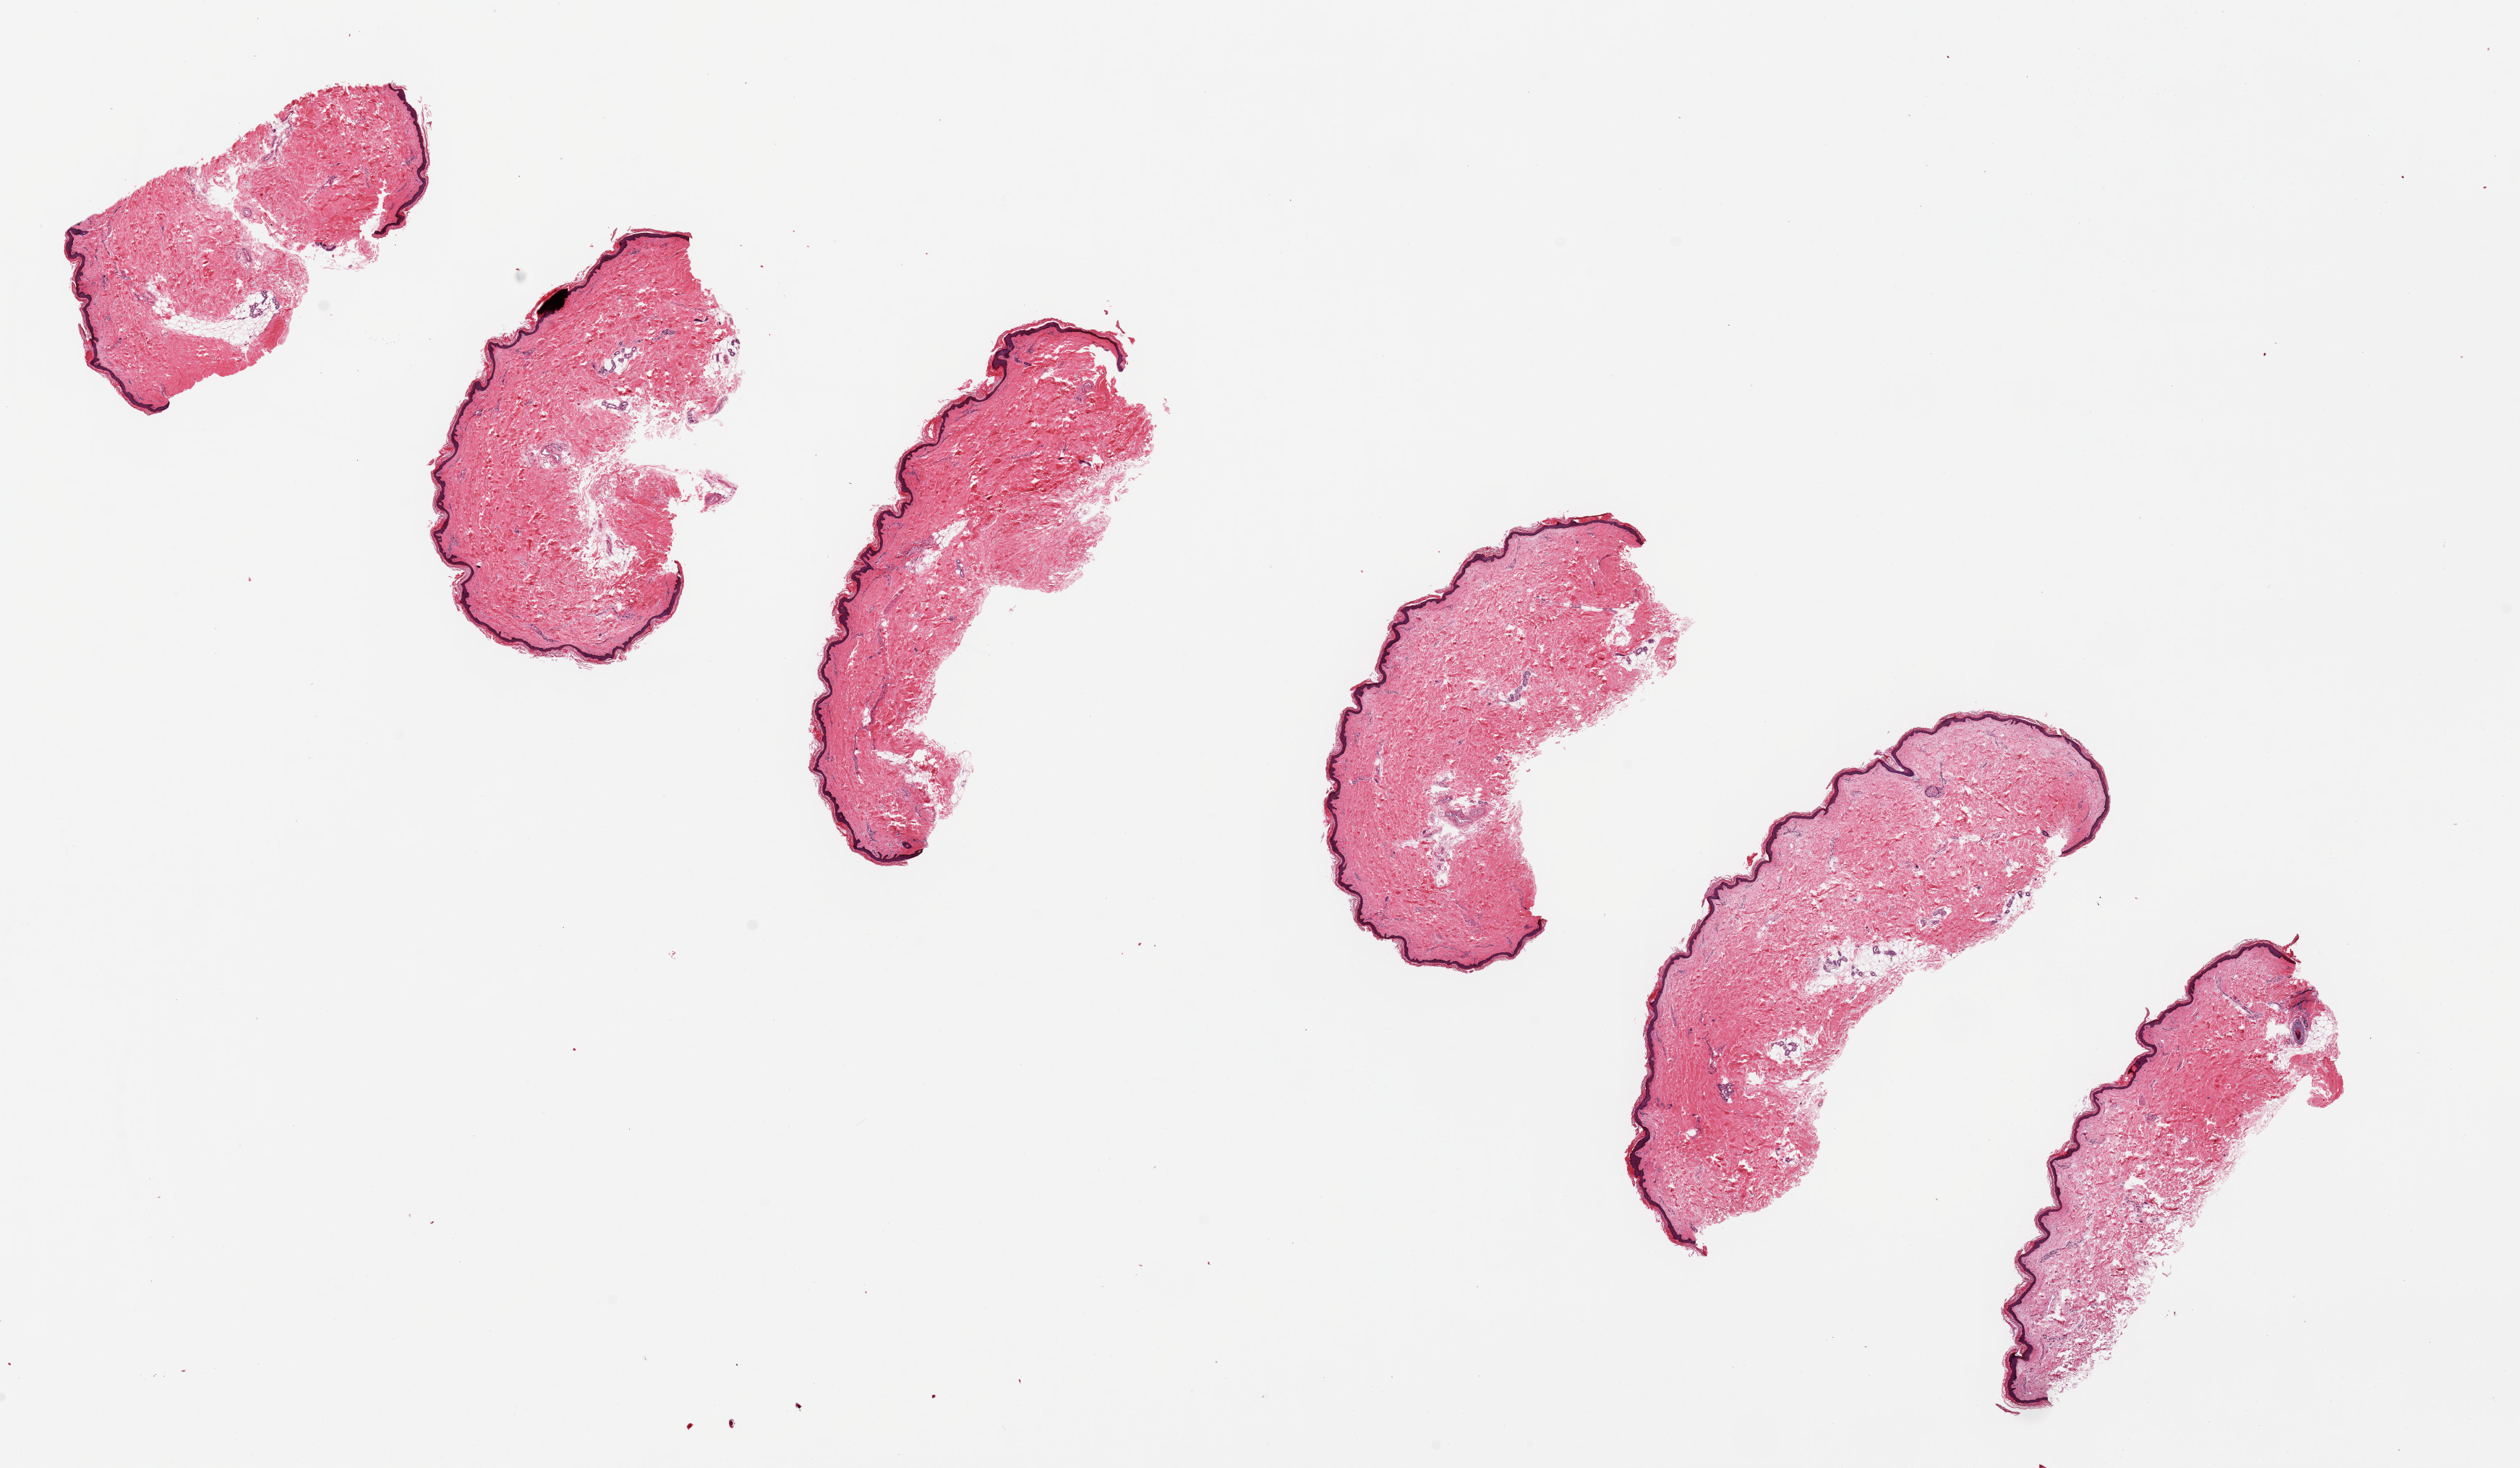
Whole-slide image, haematoxylin and eosin stain — low-resolution overview of the scanned area, about 27.6 x 16.1 mm, PAXgene-fixed paraffin-embedded (PFPE) section, target tissue: skin of lower leg, tissue donor sample.
• reviewer comment on this tissue sample: 6 ~5-6x2mm pieces. Squamous epithelium is 1-2% of thickness